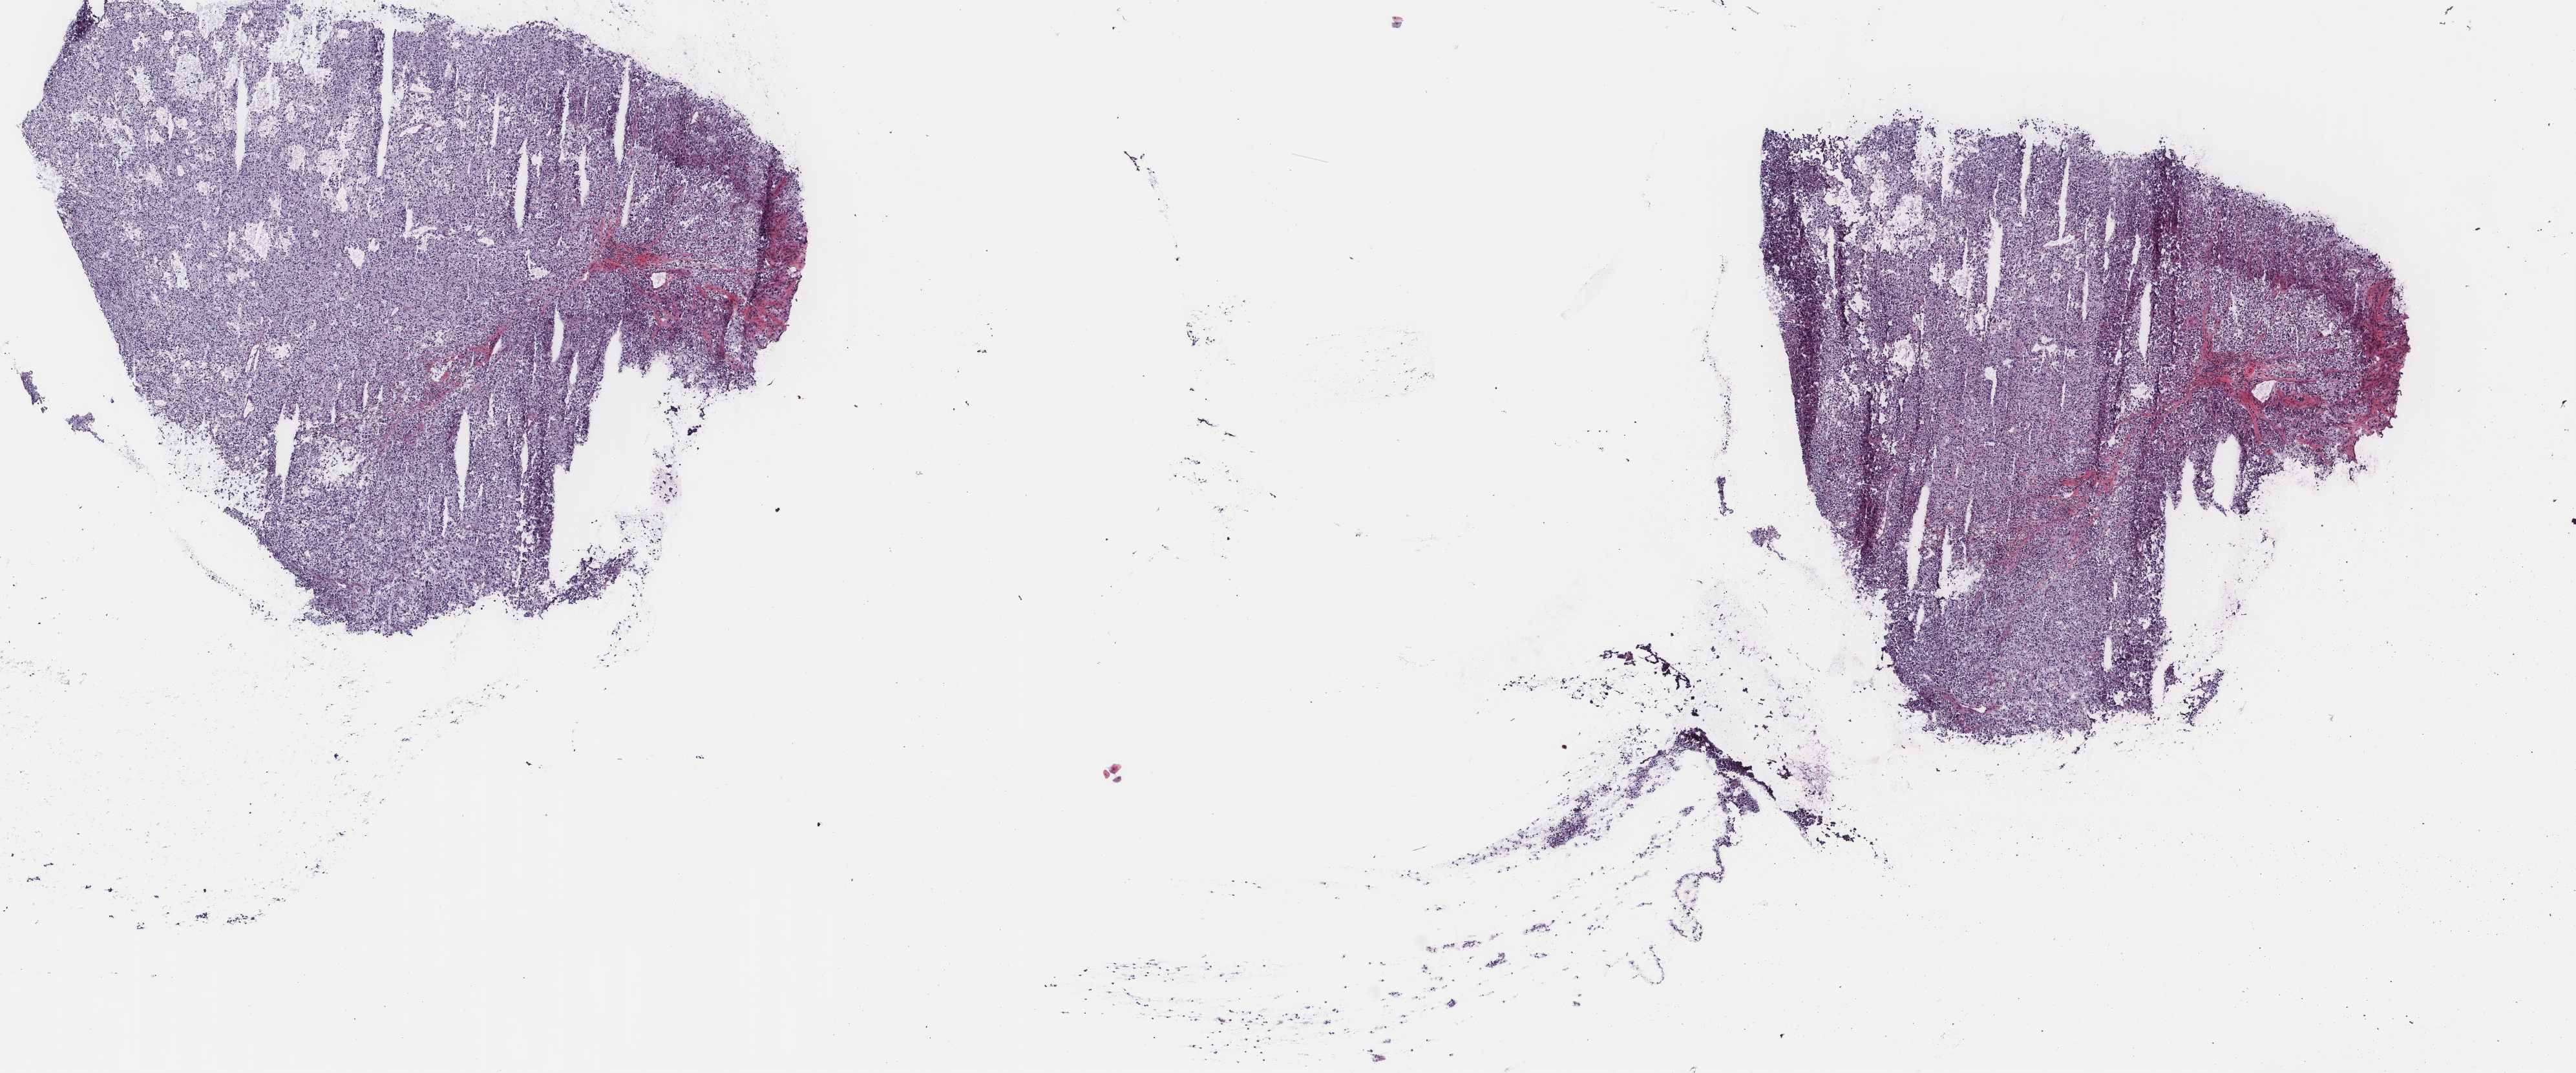
Whole-slide histology image, H&E-stained, a low-resolution overview of the entire scanned area, about 15.8 x 6.6 mm; frozen section from the top of the tissue portion; primary tumour sample from the adrenal gland. Male patient; age at initial diagnosis 40 years. Pathologist review of this section (percent, as recorded): tumour cells 95%, tumour nuclei 95%.
Pathologic diagnosis: Pheochromocytoma, malignant (medulla of adrenal gland).